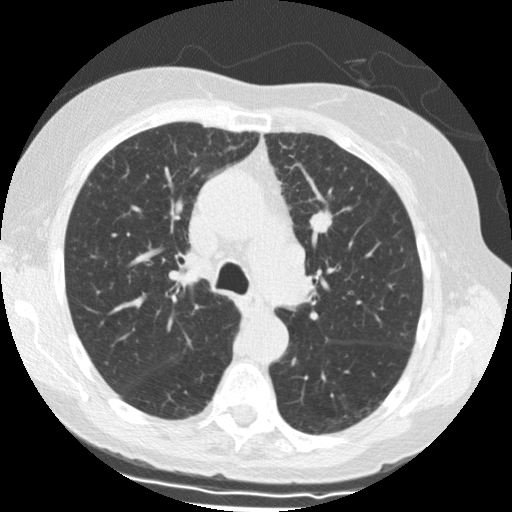
Axial slice from a low-dose chest CT screening exam; first (baseline) screen; lung window (W 1500 / L -600 HU); 2.5 mm slice thickness. Female participant, aged 69 years at enrolment. Former smoker at enrolment.
- Lesion marked by an expert reader, bounding box (x1, y1, x2, y2) in pixels: (299, 206, 345, 246).
- The screening reader recorded 2 non-calcified nodules or masses ≥4 mm on this exam; which of them this box marks is not recorded.
- Lung cancer was diagnosed 18 days after this screen: squamous cell carcinoma, NOS, left upper lobe, stage IIIA (AJCC 6th edition), 15 mm at pathology.